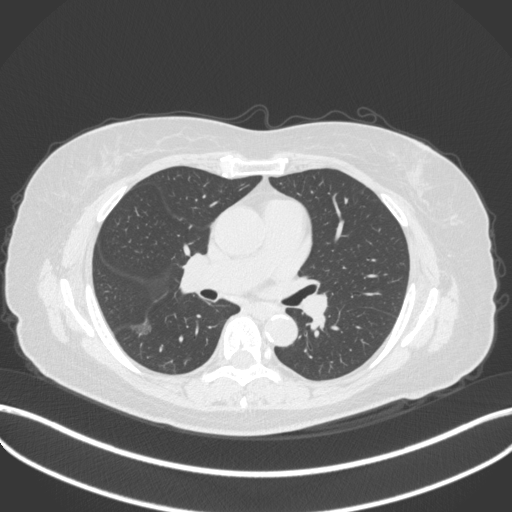
Chest CT, one axial slice. Slice 178 of 322 in the series (ordered by position). 120 kVp. Lung window (W 1500 / L -600 HU). 512 × 512 image matrix, field of view 400 × 400 mm. Female patient, age 64 years. Case-level facts recorded for this patient, not image findings: clinical TNM (as recorded): T1c N0 M0; histopathological grade: G1.
Annotated regions visible in this slice (bounding box drawn by a radiologist):
- lung tumour (recorded histology: adenocarcinoma): bounding box (x1, y1, x2, y2) in pixels: (128, 311, 157, 341)